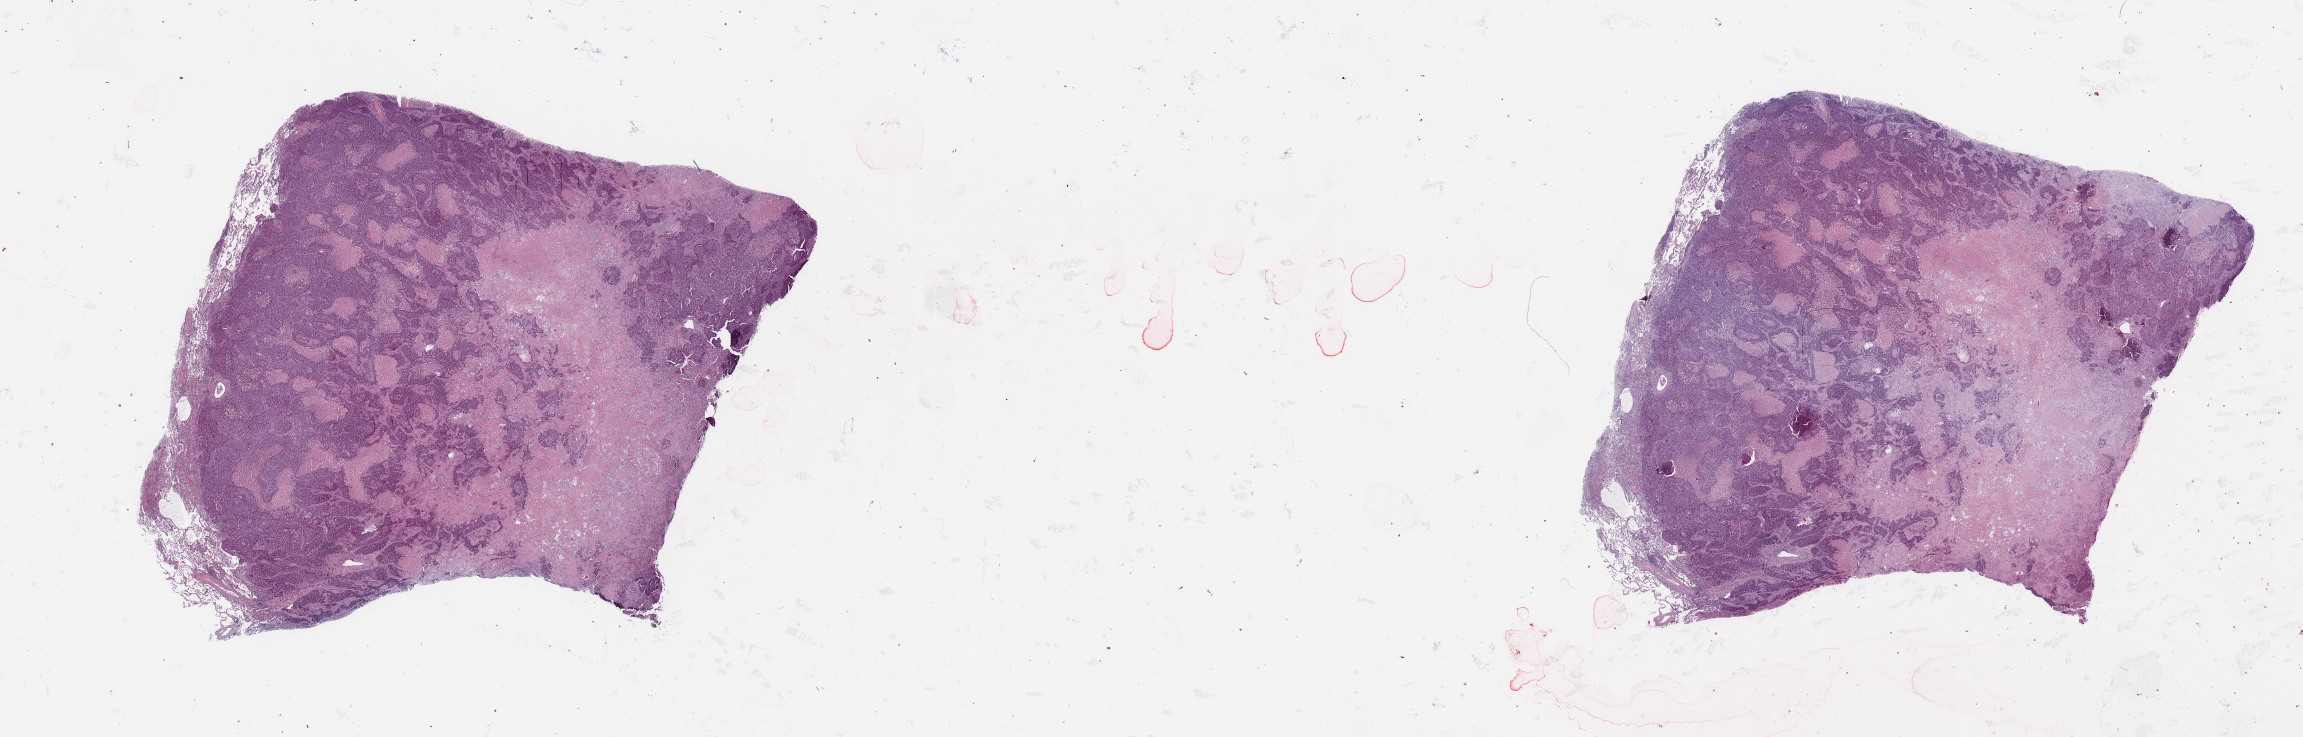
Whole-slide histology image, Hematoxylin and eosin (H&E) stained — low-resolution overview of the scanned area, about 36.4 x 11.7 mm; tumour tissue sample, lung. Male, 62 y/o. Histologic grade: G3 (poorly differentiated).
Diagnosis: Squamous cell carcinoma, NOS. Primary tumour site (as recorded): left lower lobe. AJCC pathologic stage: IIIB.